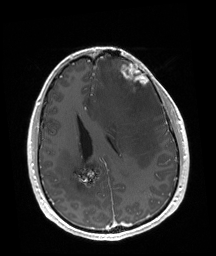
Brain MRI from a brain-tumour surgery series, one axial slice; position 70 of 192 along the scan axis; T1-weighted post-contrast; 216 × 256 image matrix, field of view 219 × 260 mm. From the clinical record (not read from this slice): tumour location: Left Frontal.
Outlined on this slice (expert manual segmentation):
- tumour: bounding box (x1, y1, x2, y2) in pixels: (121, 65, 148, 91)